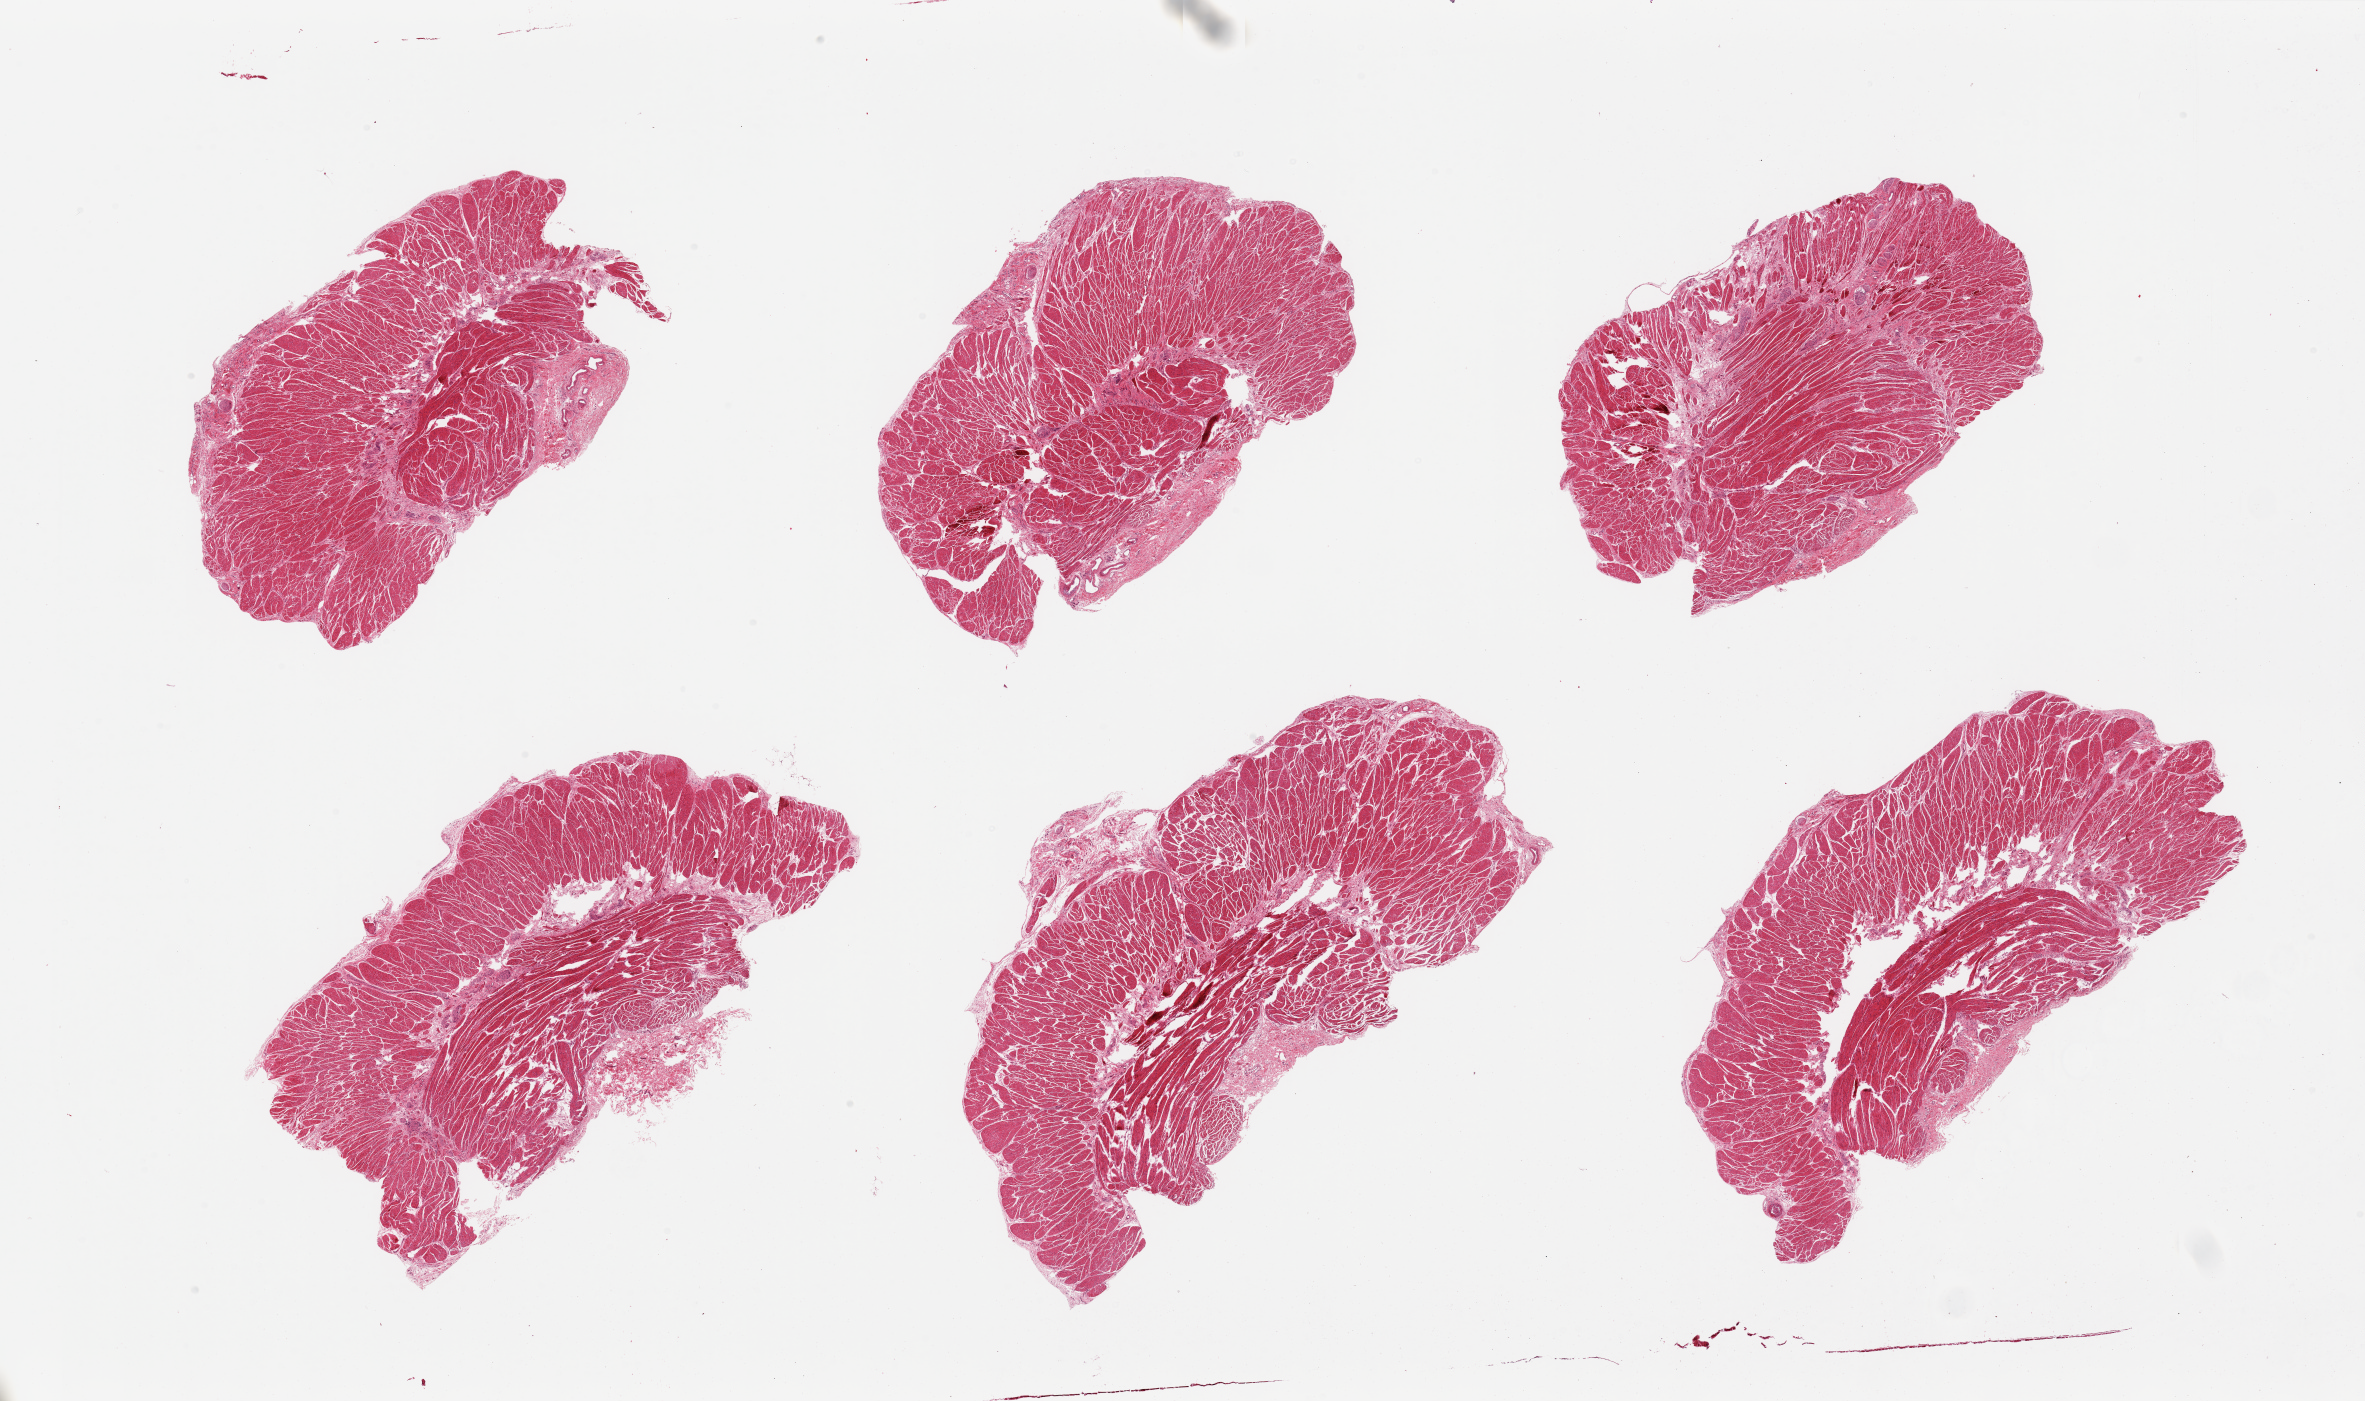
Whole-slide image, haematoxylin and eosin stain, brightfield, a low-resolution overview of the entire scanned area, about 37.4 x 22.2 mm; PAXgene-fixed paraffin-embedded (PFPE) section; target tissue: esophageal muscle; donor tissue sample. Donor sex: female.
Reviewer comment on this tissue sample: 6 pieces, well trimmed.